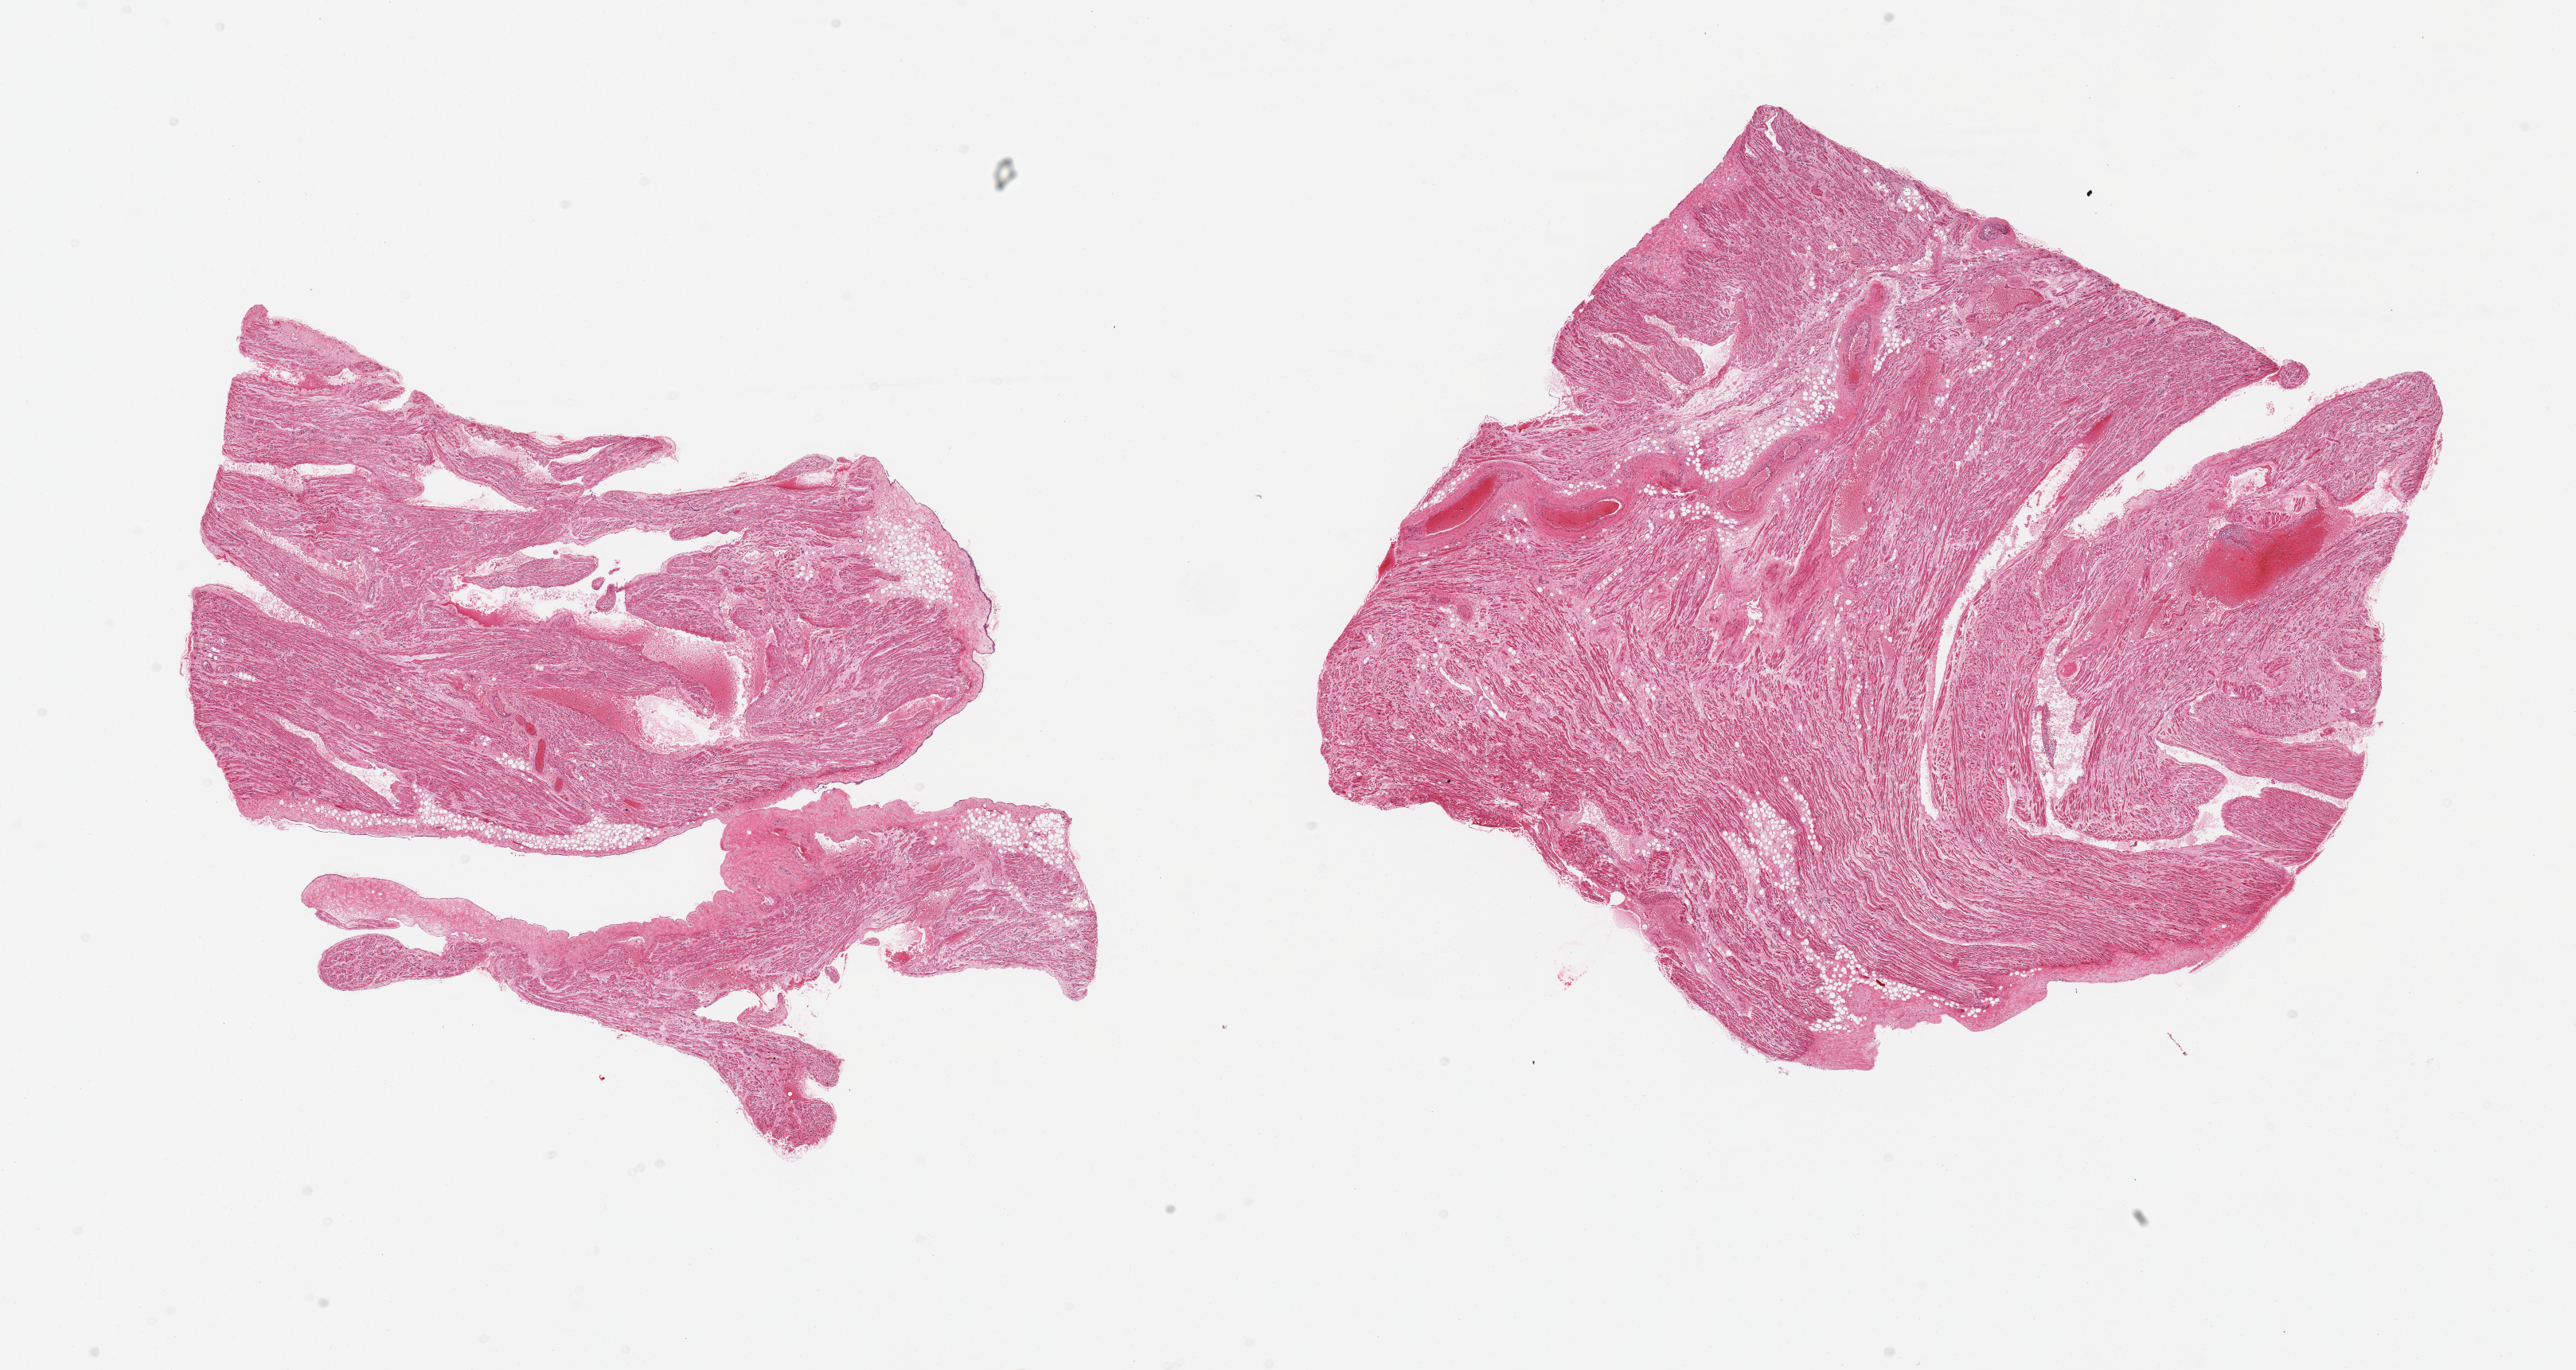
Whole-slide image, haematoxylin and eosin stain — a low-resolution overview of the entire scanned area, about 25.6 x 13.6 mm (slide scanned at 20x). PAXgene-fixed paraffin-embedded (PFPE) section. Sampled site (target tissue): auricular appendage. Donor tissue sample. Donor: male.
Pathologist's review note for this sample: 2 pieces; congested with small amount of internal fat.